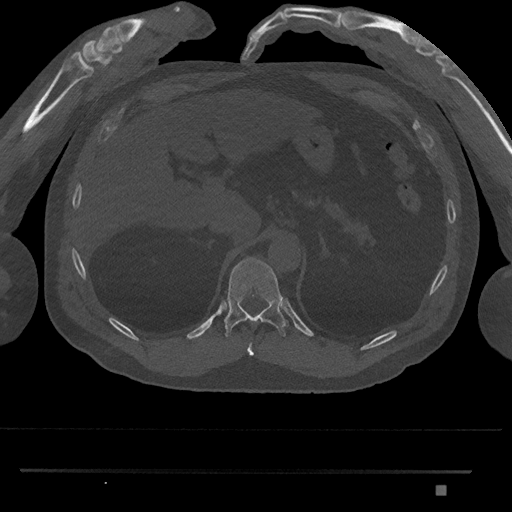
CT including the spine, one axial slice. Slice 953 of 1134 in the series (ordered by position). Reconstruction kernel Br40s/3. Bone window (W 1800 / L 400 HU). 0.5 mm slice thickness. 512 × 512 image matrix, field of view 429 × 429 mm. Patient: male, 65 years. Case-level facts recorded for this patient, not image findings: primary cancer: prostate.
Structures marked on this image (semi-automatic segmentation, software-assisted and operator-edited):
- T10 vertebra: box from (x=247, y=343) to (x=254, y=356) px
- T11 vertebra: (x=224, y=257)–(x=289, y=337)